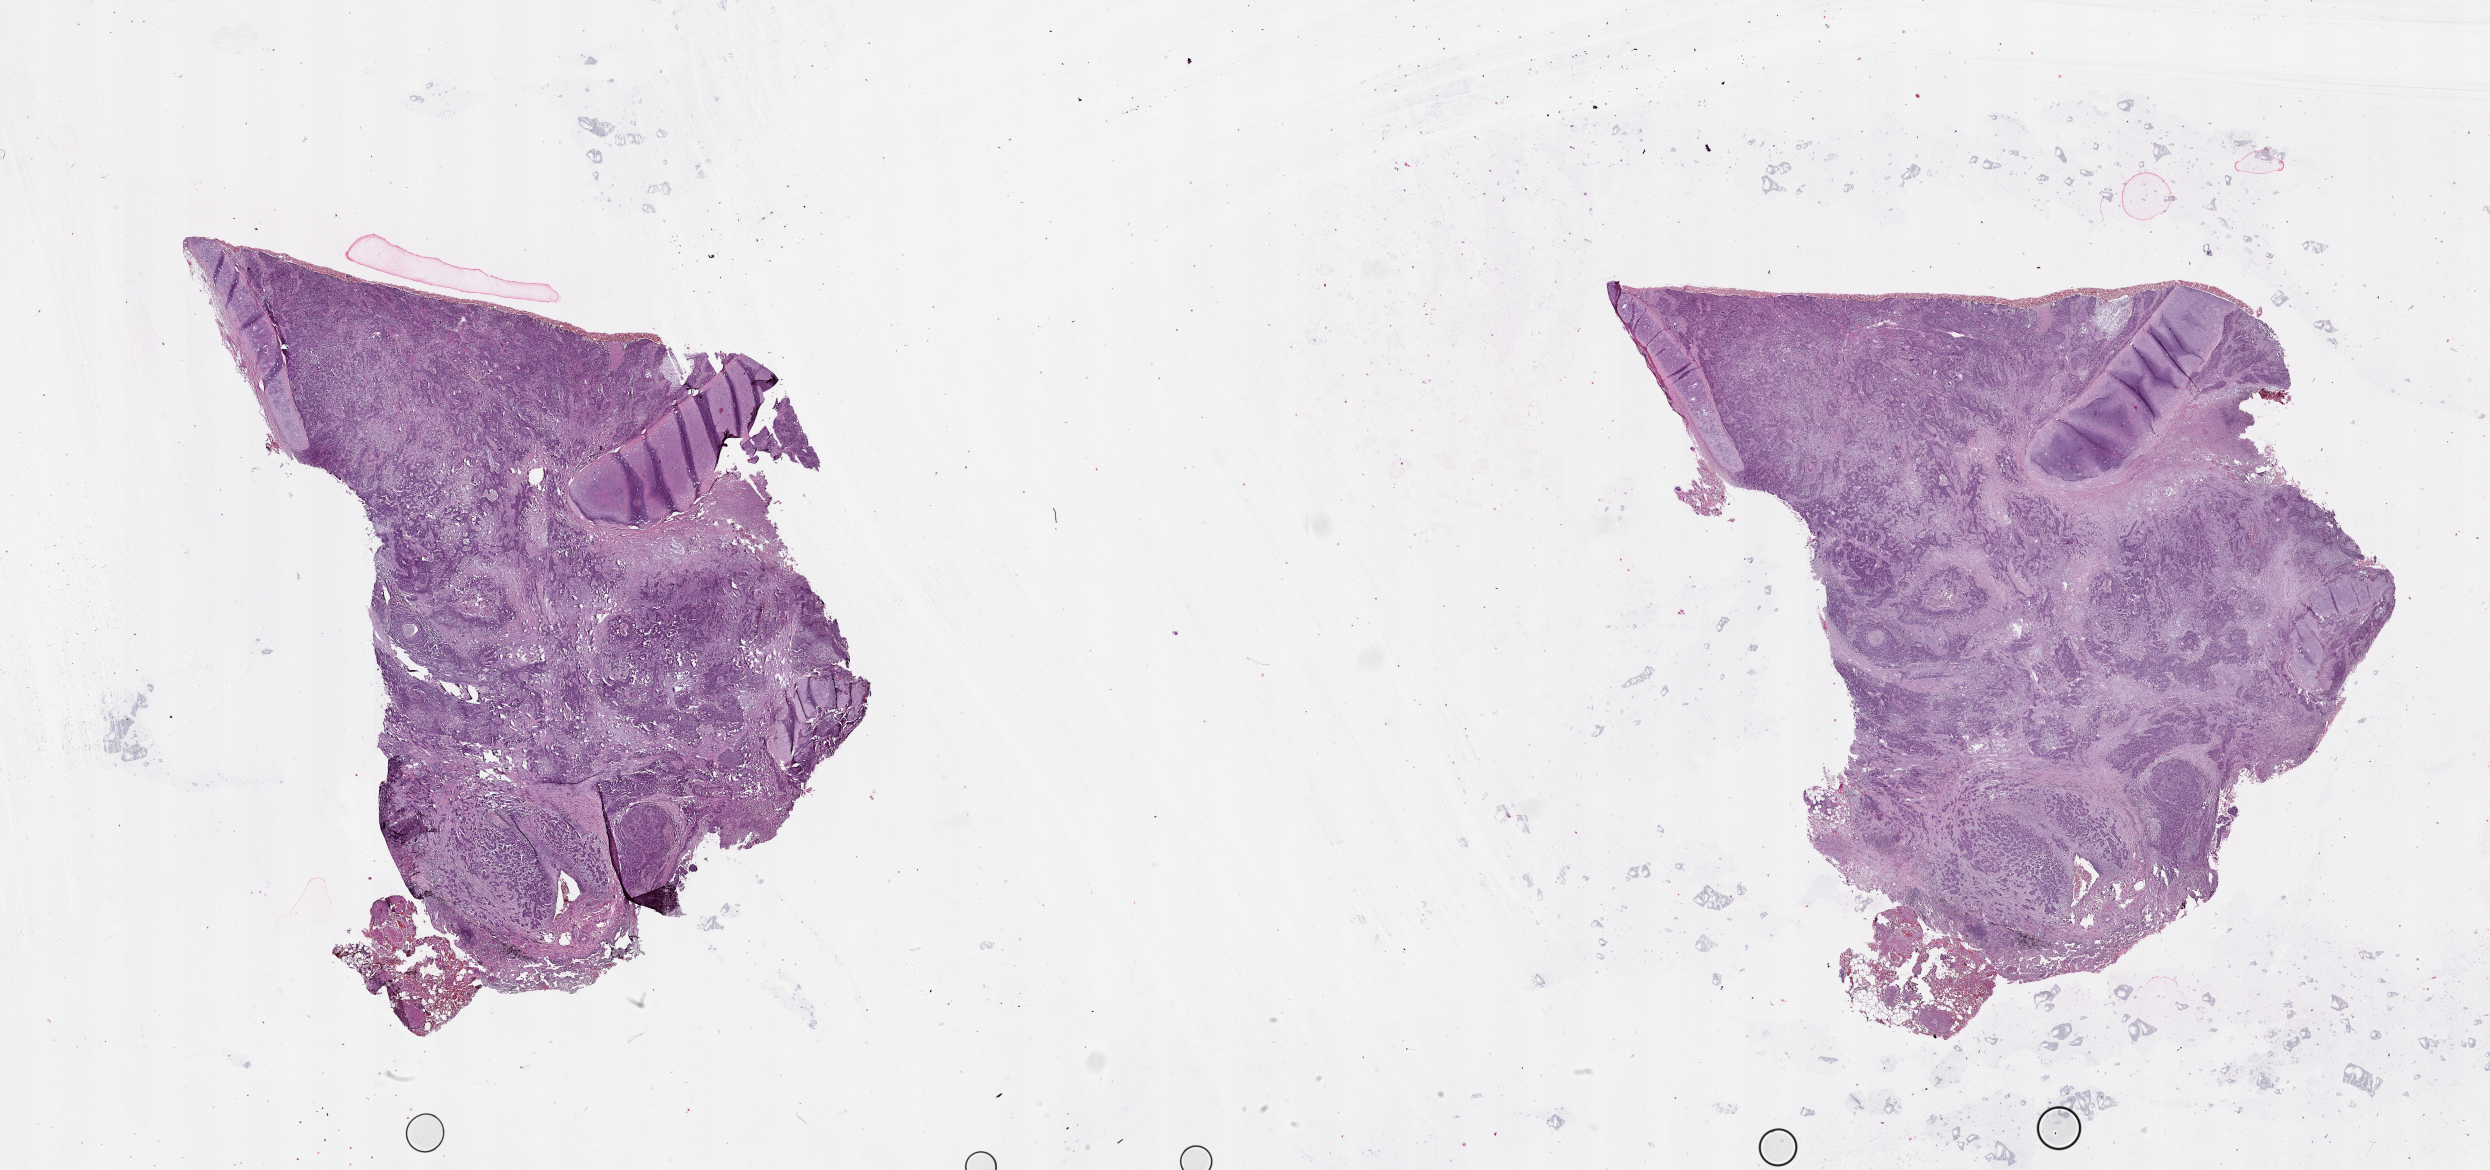
Digitized H&E tissue section (whole slide) — a low-resolution overview of the entire scanned area, about 40.1 x 18.8 mm (from a 20x scan). Lung, tumour tissue. 58-year-old male patient.
Patient diagnosis (cohort enrolment): squamous cell carcinoma (lung).